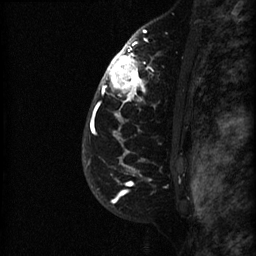
Breast MRI (dynamic contrast-enhanced), one sagittal slice; slice 51 of 60 in the series (ordered by position); dynamic contrast-enhanced series, image 2 of 3 at this slice position (ordered by acquisition); 1.5 T; TE 4.2 ms, TR 22.7 ms; 1.5 mm slice thickness; 256 × 256 image matrix. Female patient, age 48 years. From the clinical record (not read from this slice): setting: breast cancer imaged before/during neoadjuvant chemotherapy; receptor status: triple-negative.
Outlined on this slice (semi-automatically segmented with operator editing):
- analysis volume of interest (the breast-tissue region the enhancement analysis was run in; not a lesion): box from (x=89, y=27) to (x=191, y=180) px
- tumour enhancement mask (voxels above the 90 % enhancement threshold inside the analysis volume of interest): (x=91, y=30)–(x=150, y=170)